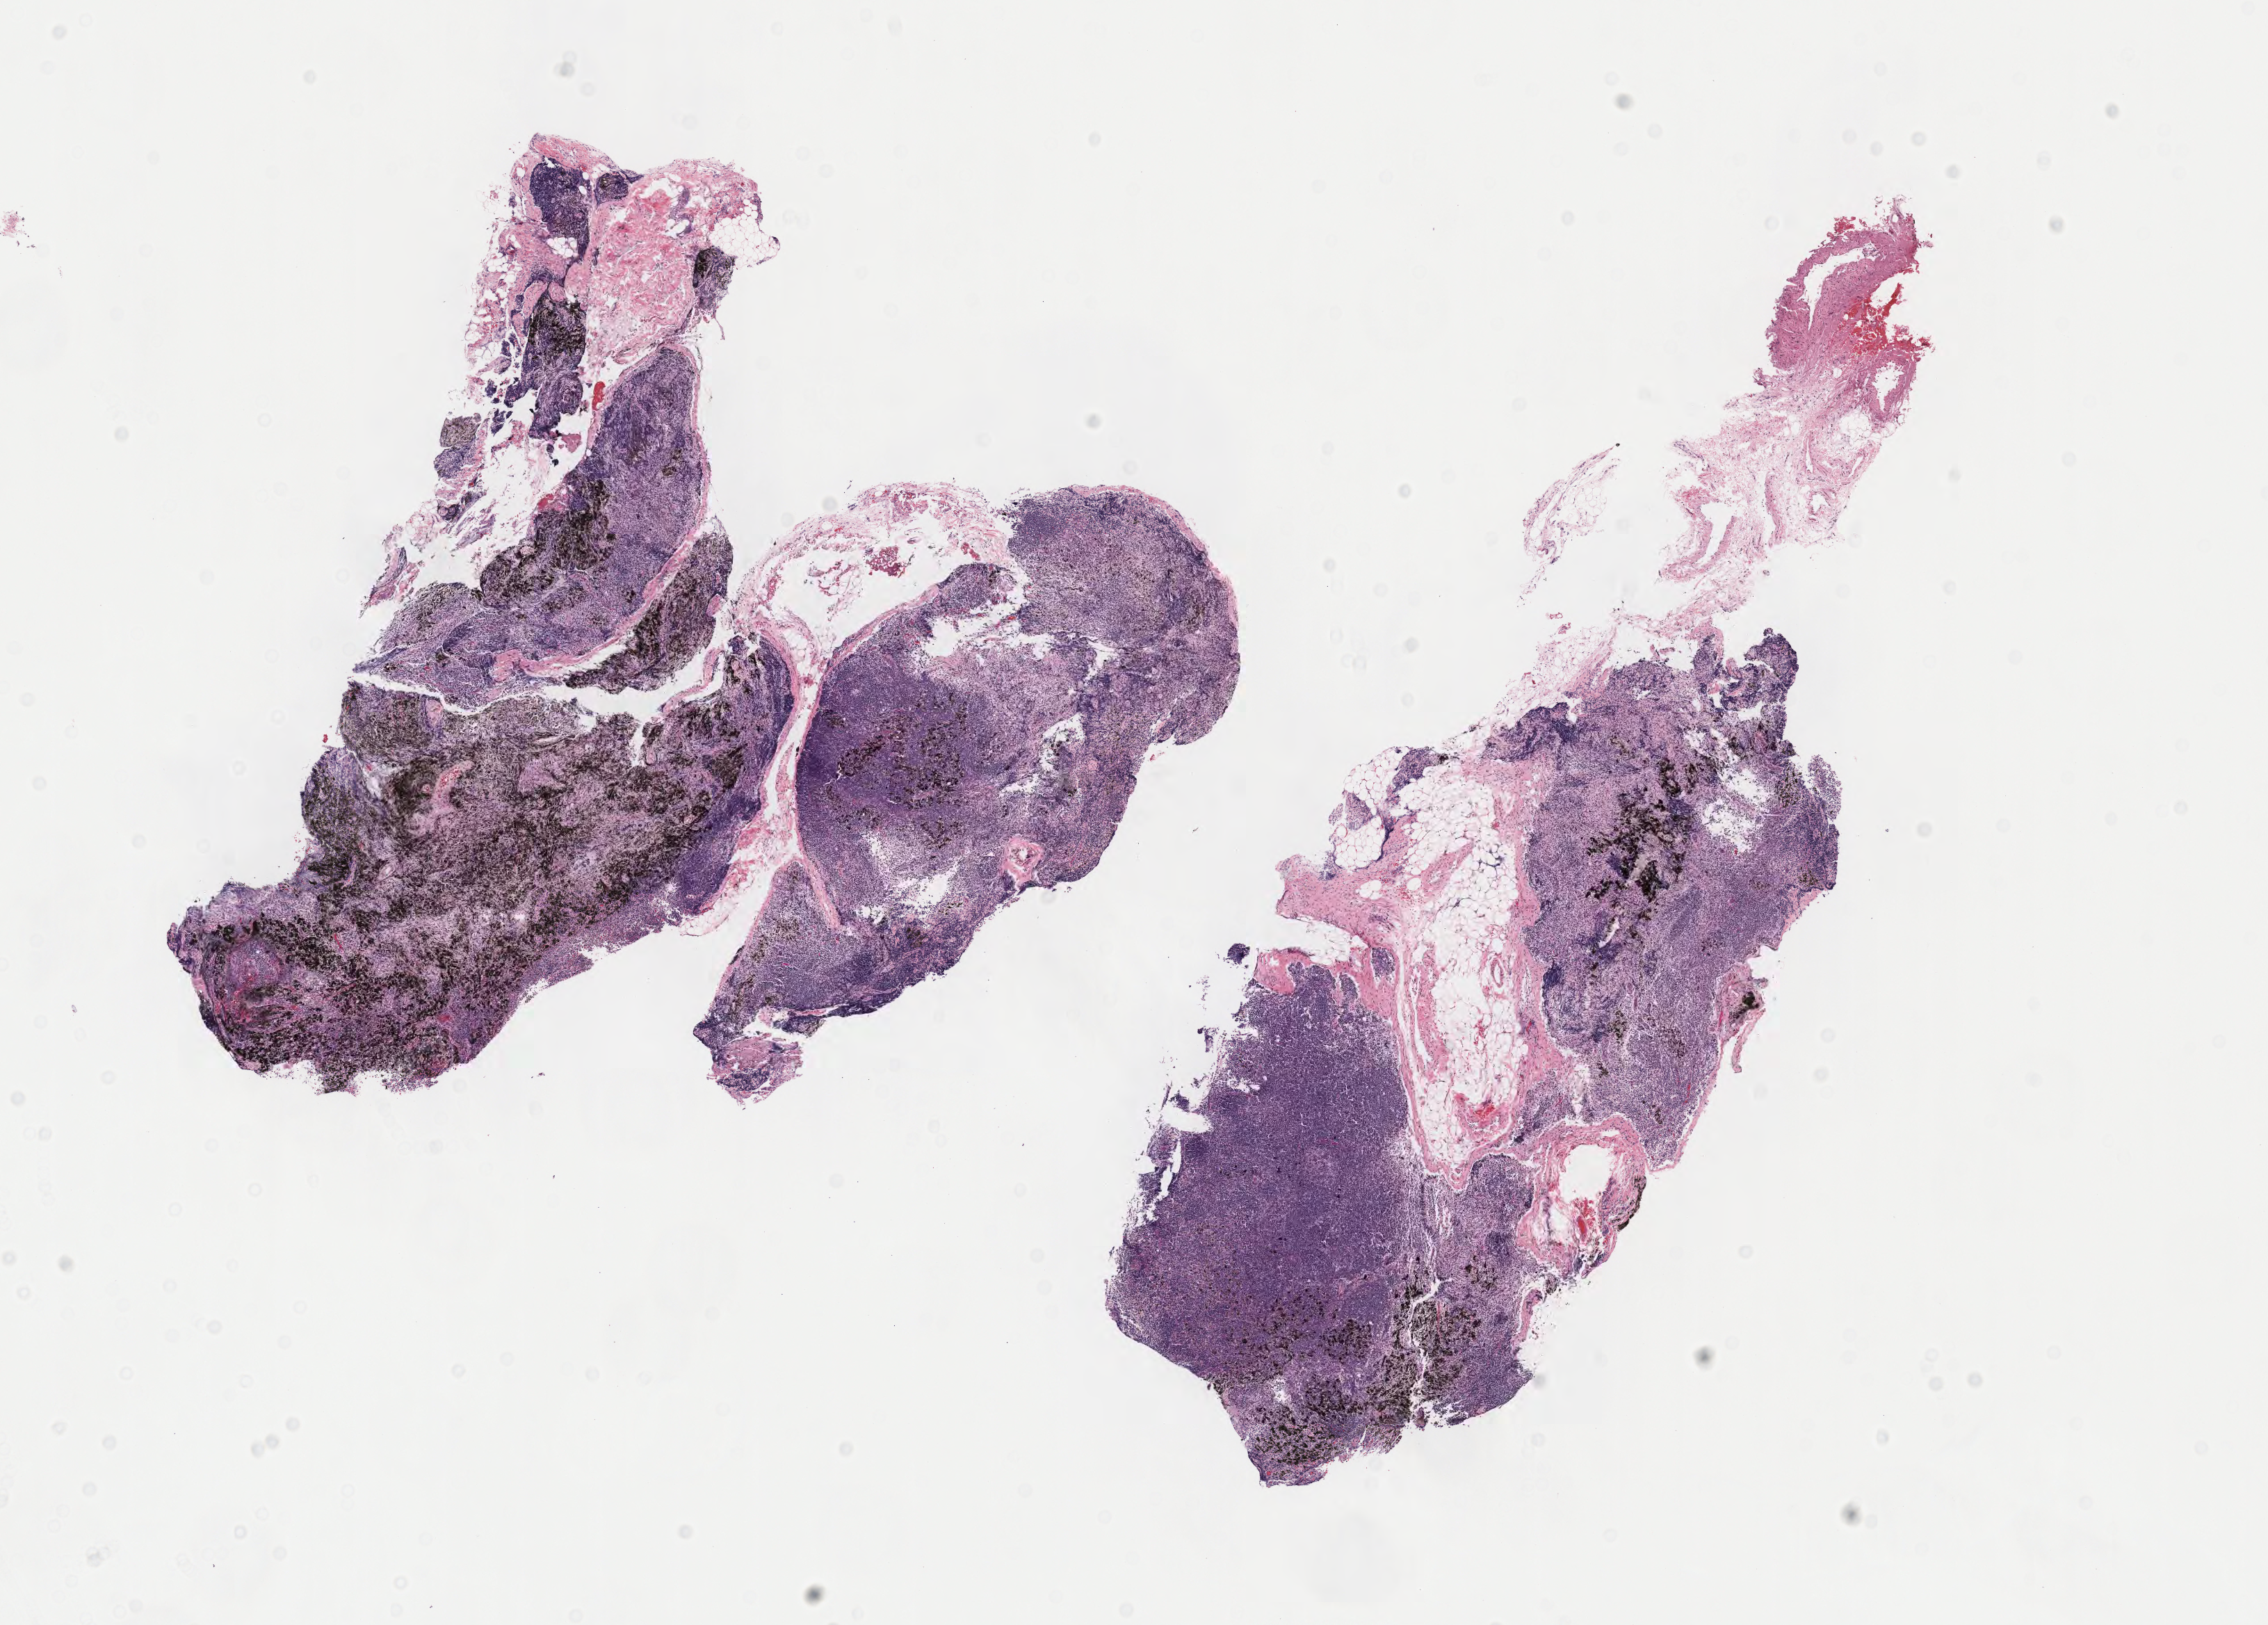
Whole-slide histology image, H&E-stained, a low-resolution overview of the entire scanned area, about 12.9 x 9.3 mm; formalin-fixed paraffin-embedded (FFPE) diagnostic section; primary tumour sample from the thymus. Patient: female, age at initial diagnosis 43 years.
Histologic diagnosis: Thymoma, type B2, malignant.